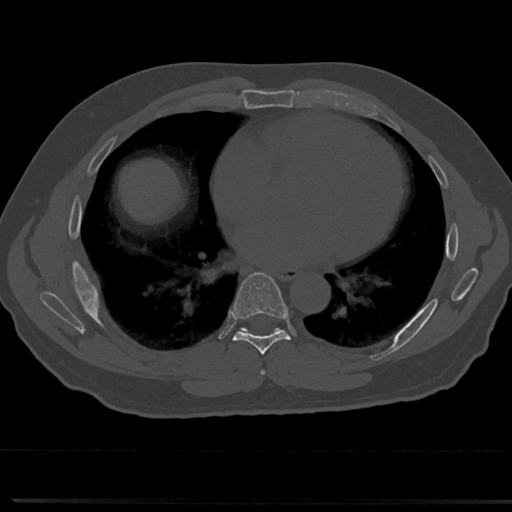
CT including the spine, one axial slice. Reconstruction kernel Br40s/3. Bone window (W 1800 / L 400 HU). 0.5 mm slice thickness. 512 × 512 image matrix, field of view 355 × 355 mm. Male patient, age 61 years. Case-level facts recorded for this patient, not image findings: primary cancer: prostate.
Outlined on this slice (semi-automatically segmented with operator editing):
- T6 vertebra: bounding box <261,340,319,376> (left, top, right, bottom; pixels)
- T7 vertebra: <214,275,310,358>